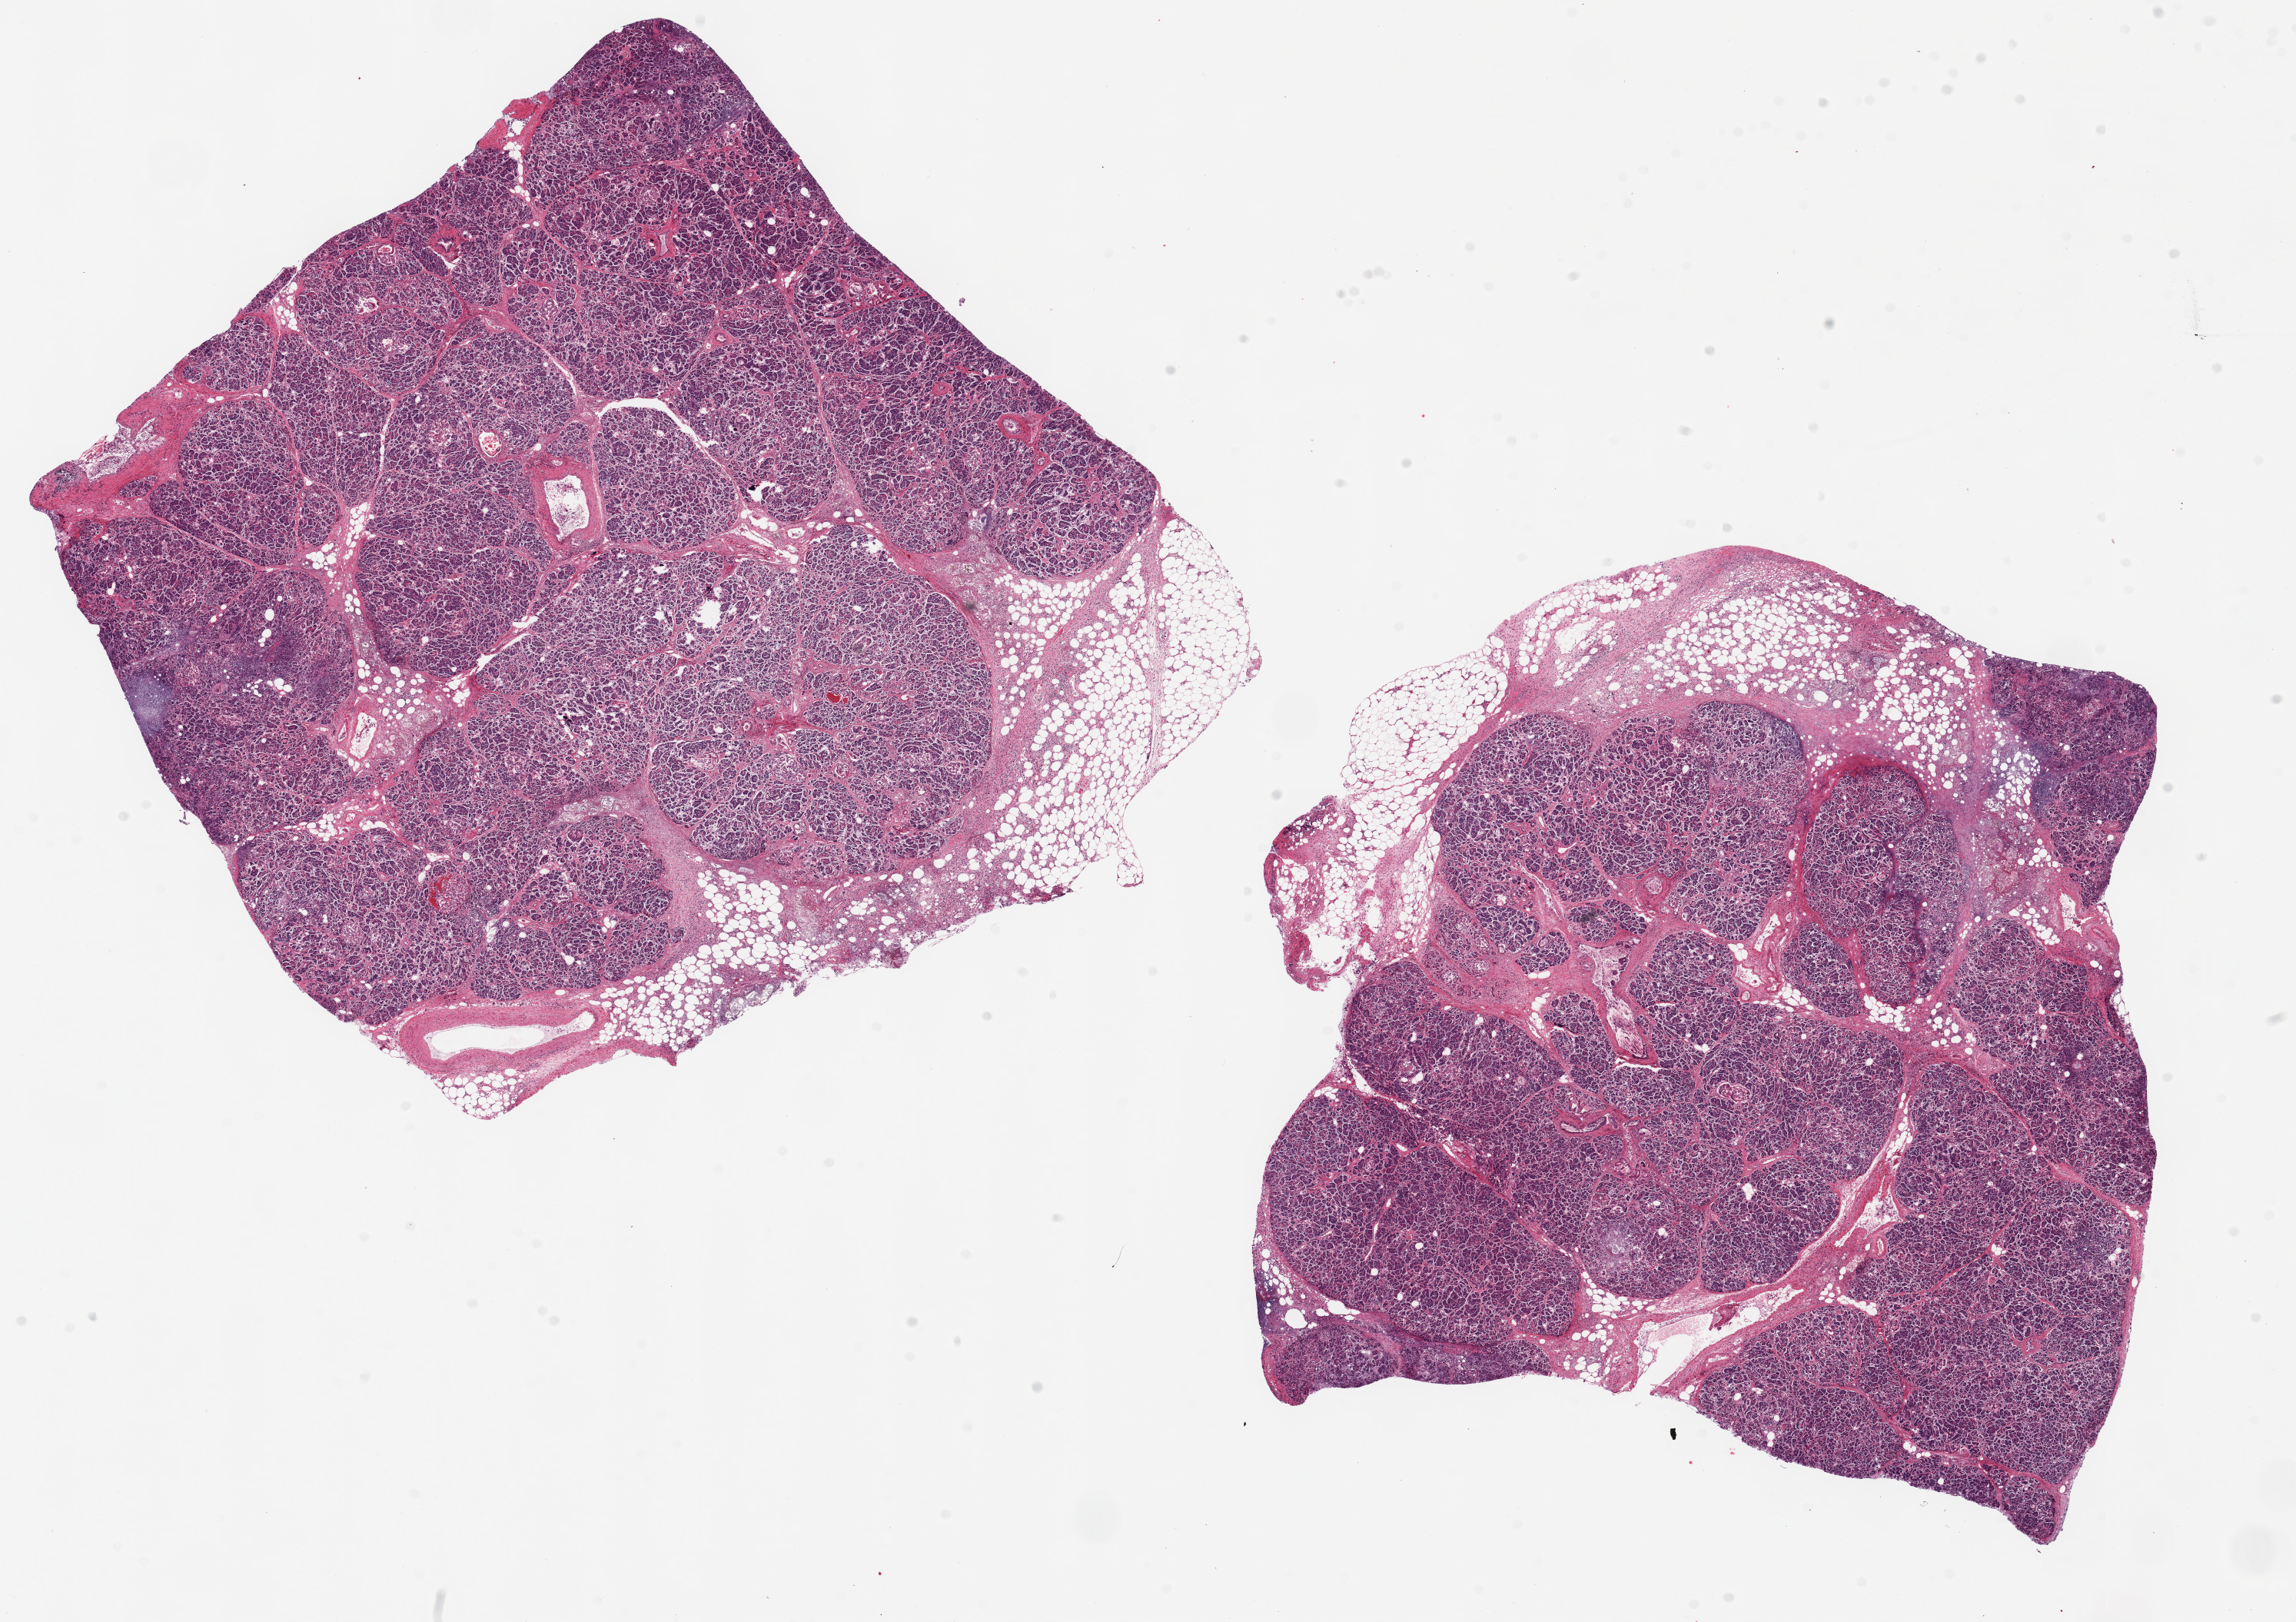
Hematoxylin and eosin (H&E) whole-slide image, brightfield — shown as a low-resolution overview of the whole scanned area (about 23.6 x 16.7 mm, from a 20x scan), PAXgene-fixed, paraffin-embedded tissue, sampled site (target tissue): pancreas, tissue donor sample. Donor sex: male.
Review note (as recorded): 2 ~9x8mm aliquots, extensive peri-and intra-pancreatic saponification.